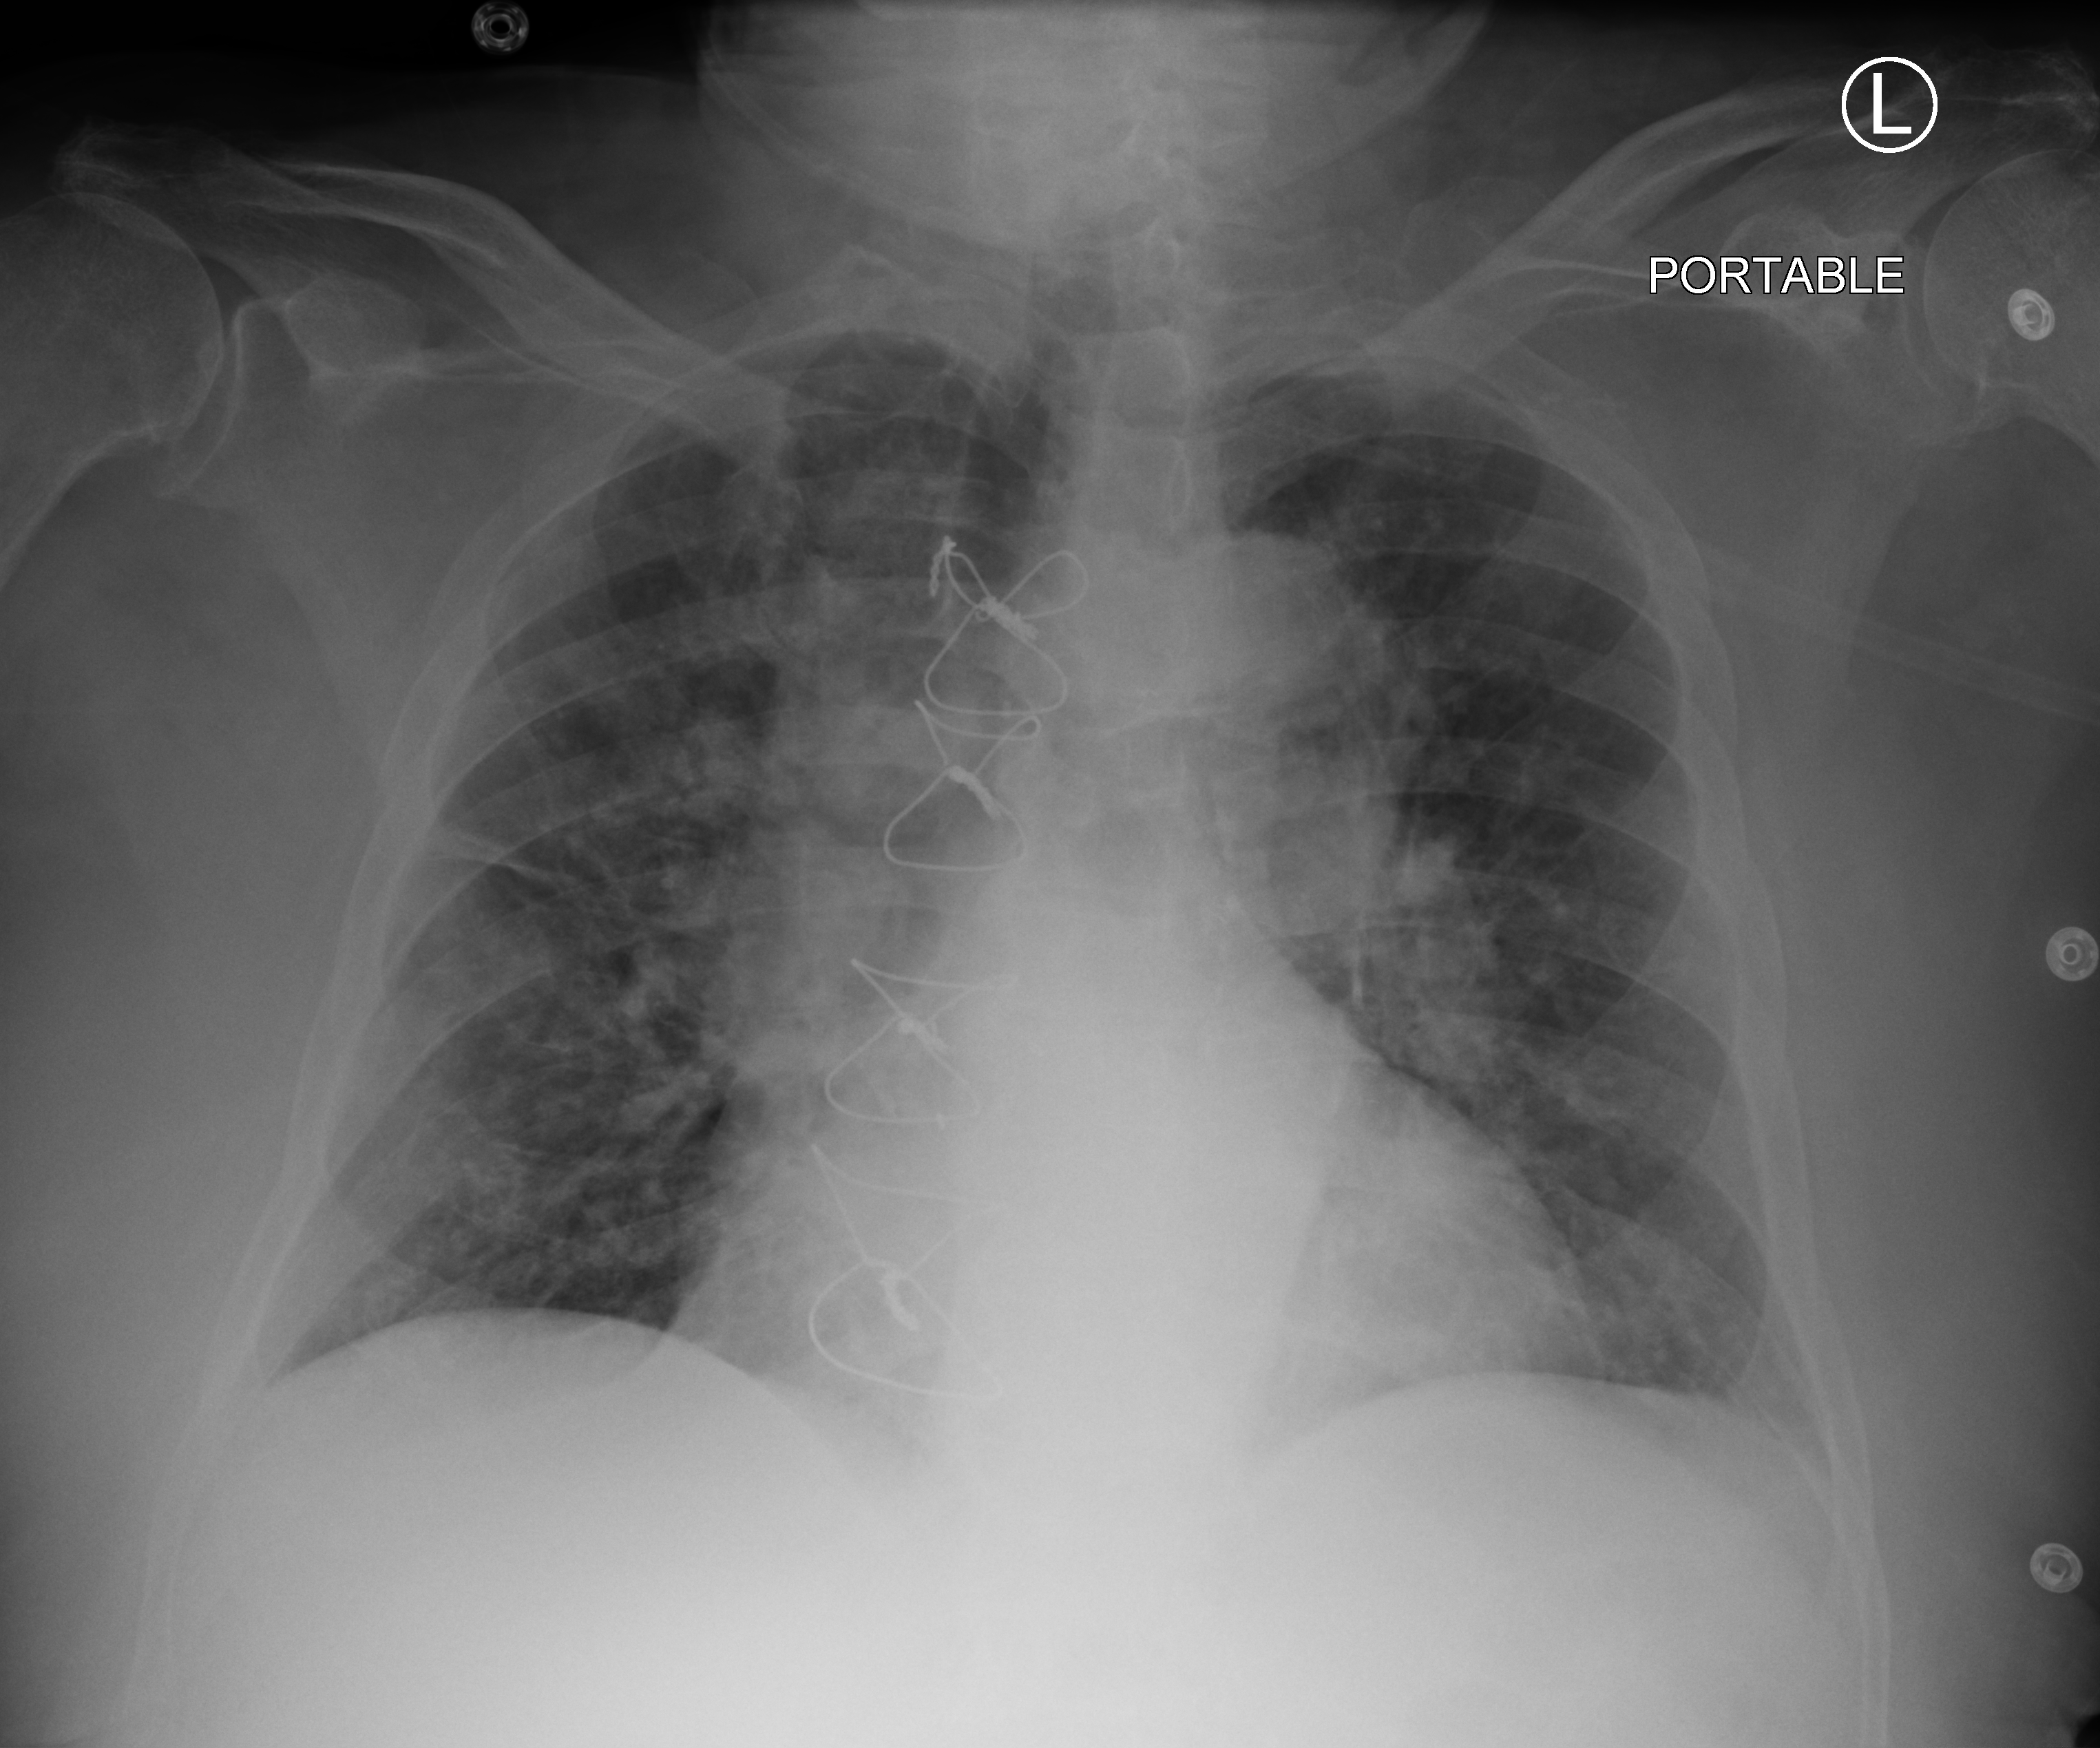
Chest X-ray (portable); anteroposterior (AP) projection. Patient hospitalised with COVID-19; male, aged 75–90 years.
Admission-level facts for this patient (not findings on this image; timing relative to this image not recorded): other chronic lung disease (admission record): no.